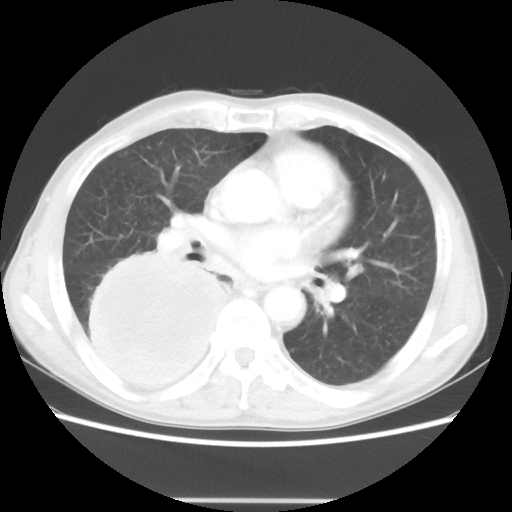
Chest CT, one axial slice; lung window (W 1500 / L -600 HU); 5 mm slice thickness; 512 × 512 image matrix, field of view 361 × 361 mm. Male patient, age 66 years. From the clinical record (not read from this slice): clinical TNM (as recorded): T4 N1 M1; histopathological grade: G3.
Outlined on this slice (rectangle marked by the reading radiologist):
- lung tumour (recorded histology: small cell carcinoma): bounding box [x1, y1, x2, y2] px = [84, 252, 227, 394]